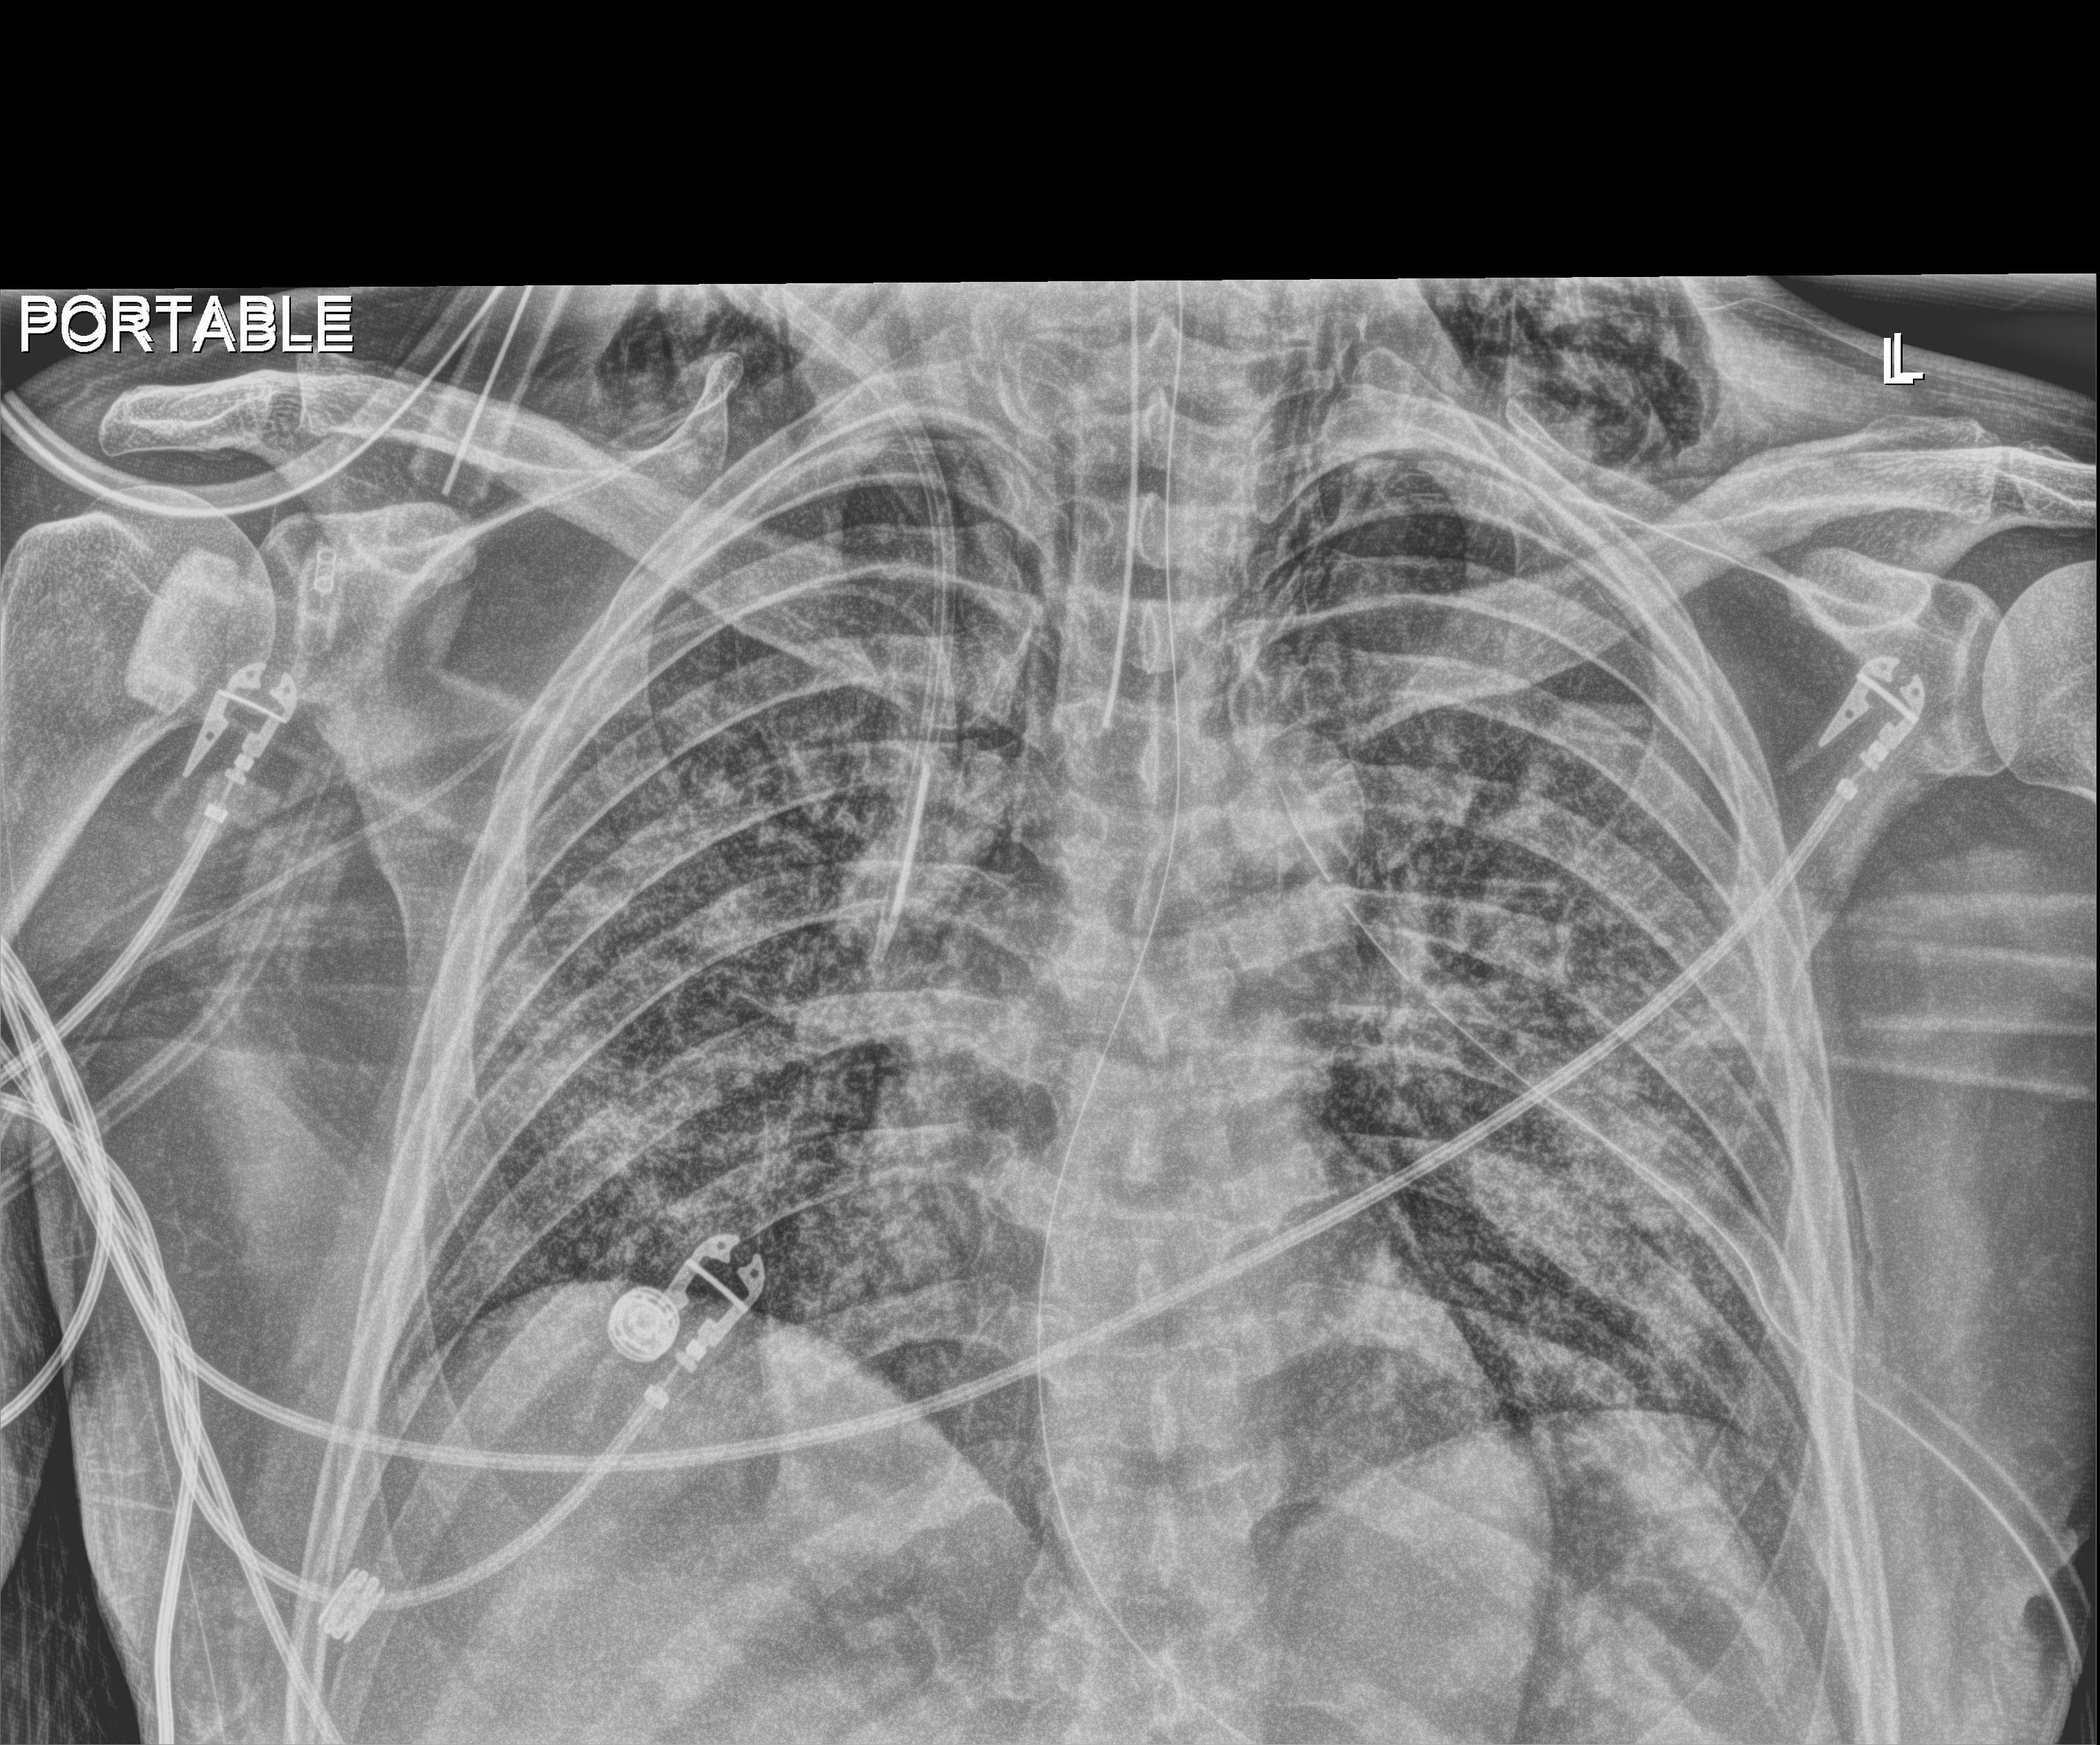
Chest X-ray (portable); anteroposterior (AP) projection. Patient hospitalised with COVID-19; male, aged 18–59 years.
Admission-level facts for this patient (not findings on this image; timing relative to this image not recorded):
- mechanically ventilated during this hospital stay: yes
- admitted to intensive care during this hospital stay: yes